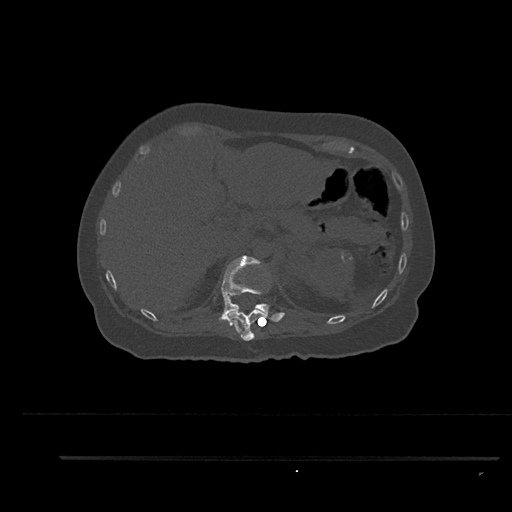
CT including the spine, one axial slice. Position 288 of 797 along the scan axis. 120 kVp. Bone window (W 1800 / L 400 HU). 0.5 mm slice thickness. 512 × 512 image matrix, field of view 408 × 408 mm. Female patient, age 44 years. Case-level facts recorded for this patient, not image findings: primary cancer: renal; vertebrae with lytic lesions (as recorded): L1.
Outlined on this slice (semi-automatic segmentation, software-assisted and operator-edited):
- T11 vertebra: box from (x=230, y=308) to (x=265, y=341) px
- T12 vertebra: (x=219, y=255)–(x=285, y=322)